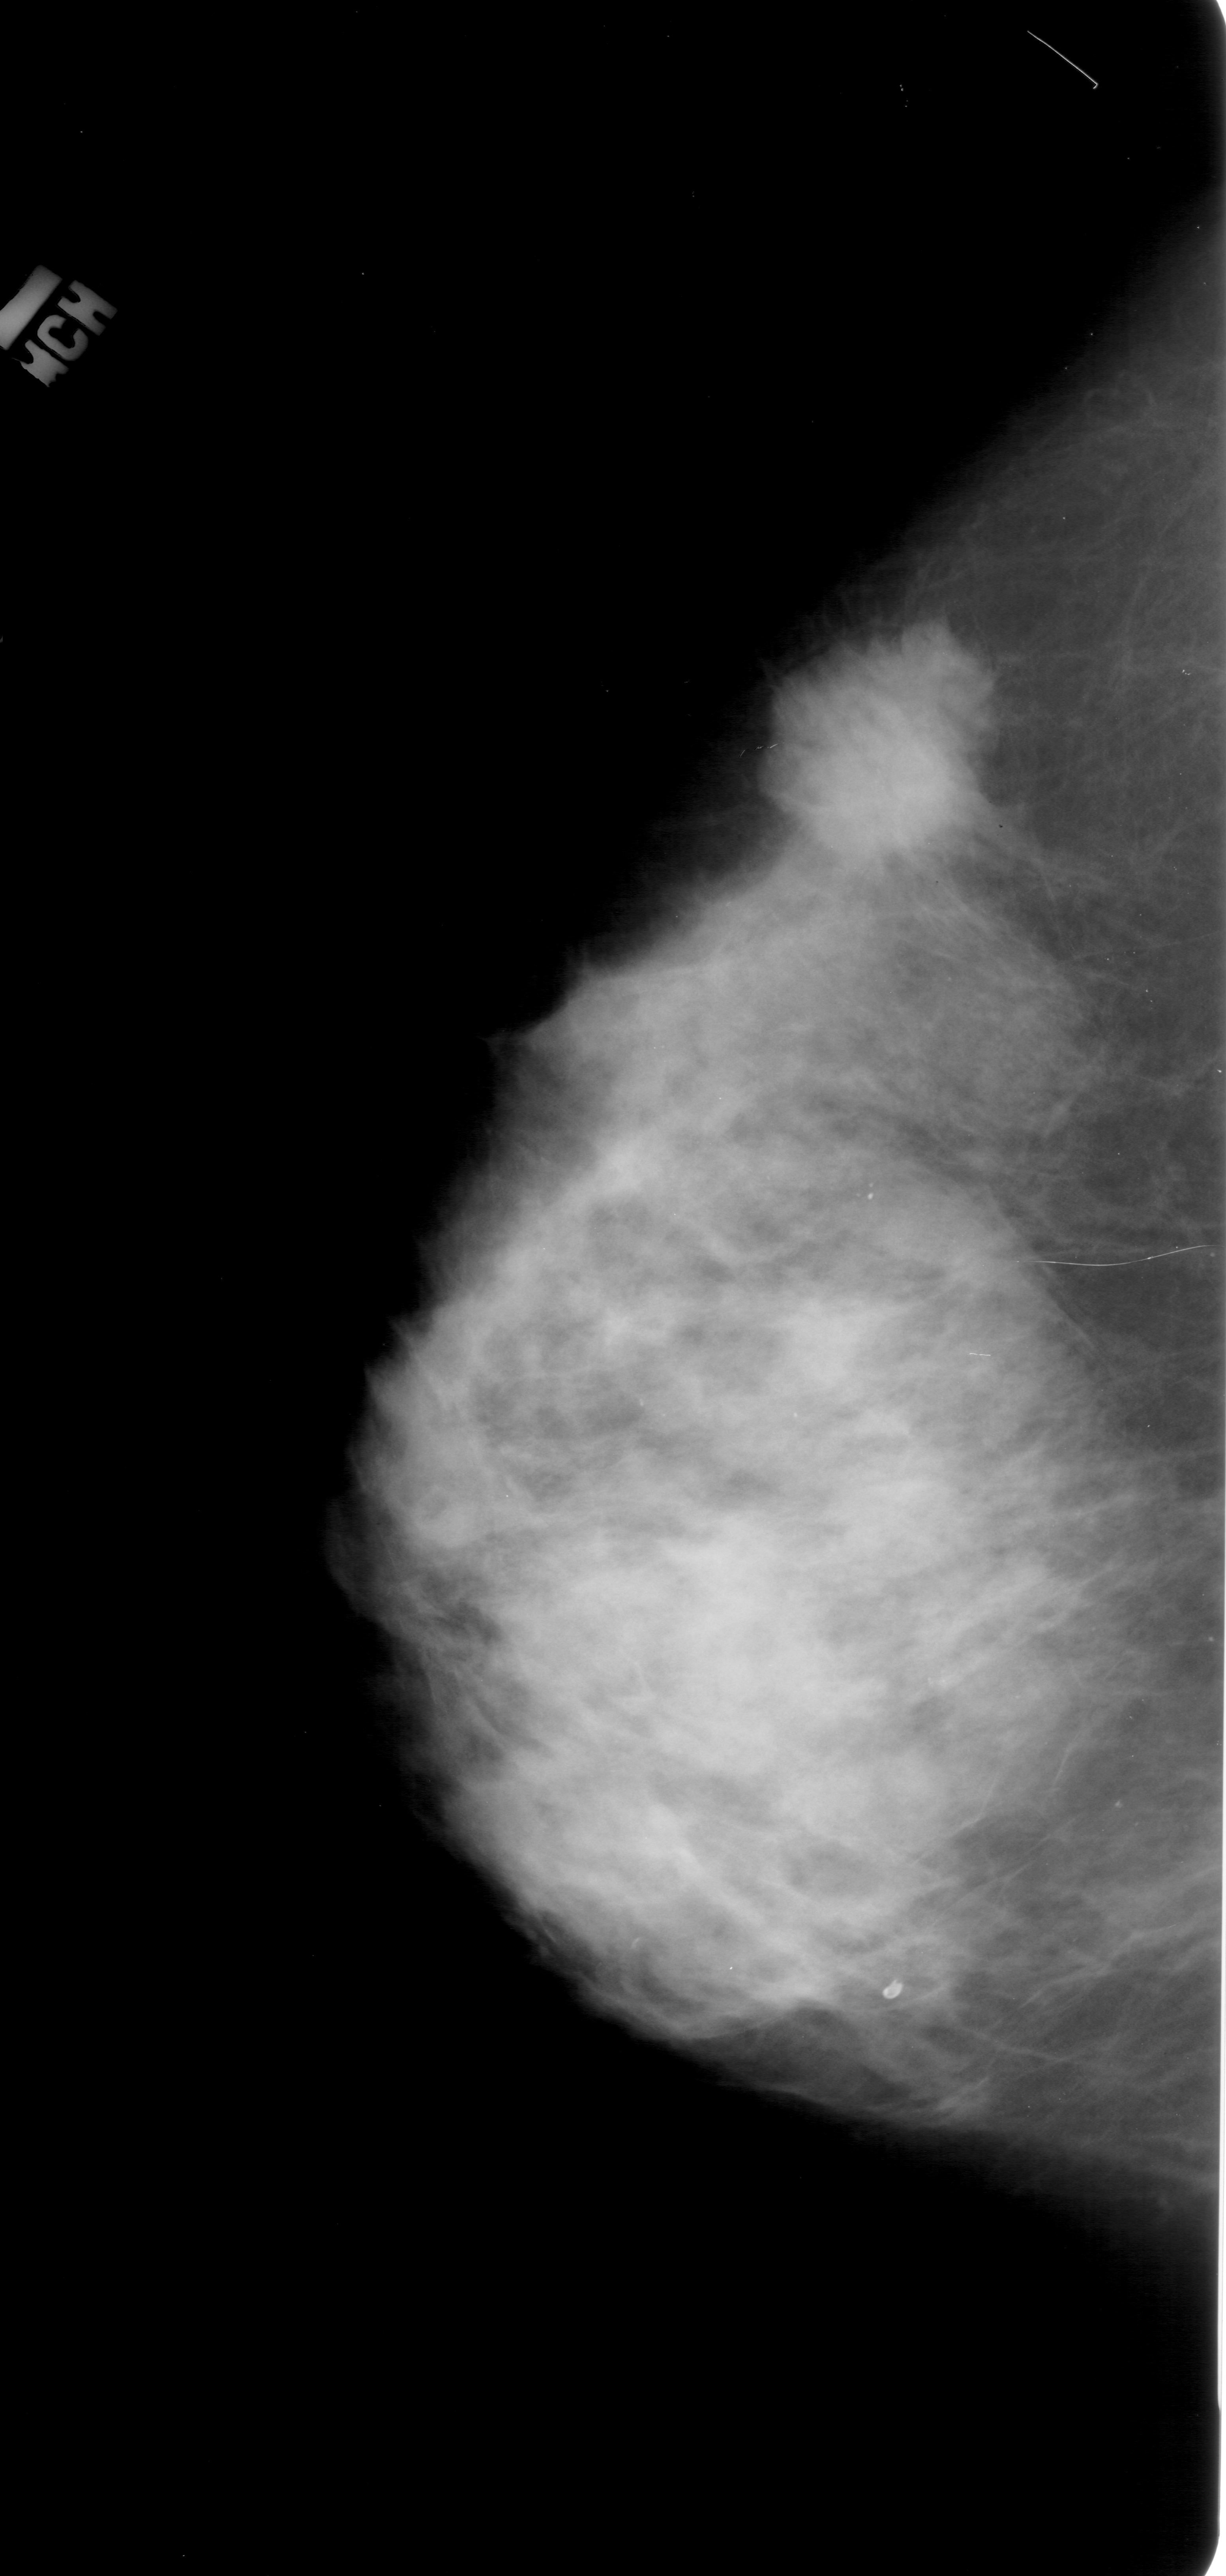
Digitized screen-film mammogram; left breast; CC view; breast composition: extremely dense (BI-RADS density category 4 of 4).
Mass, shape irregular, margins spiculated; BI-RADS assessment category 5; pathology result (as recorded, not read from the image): malignant.